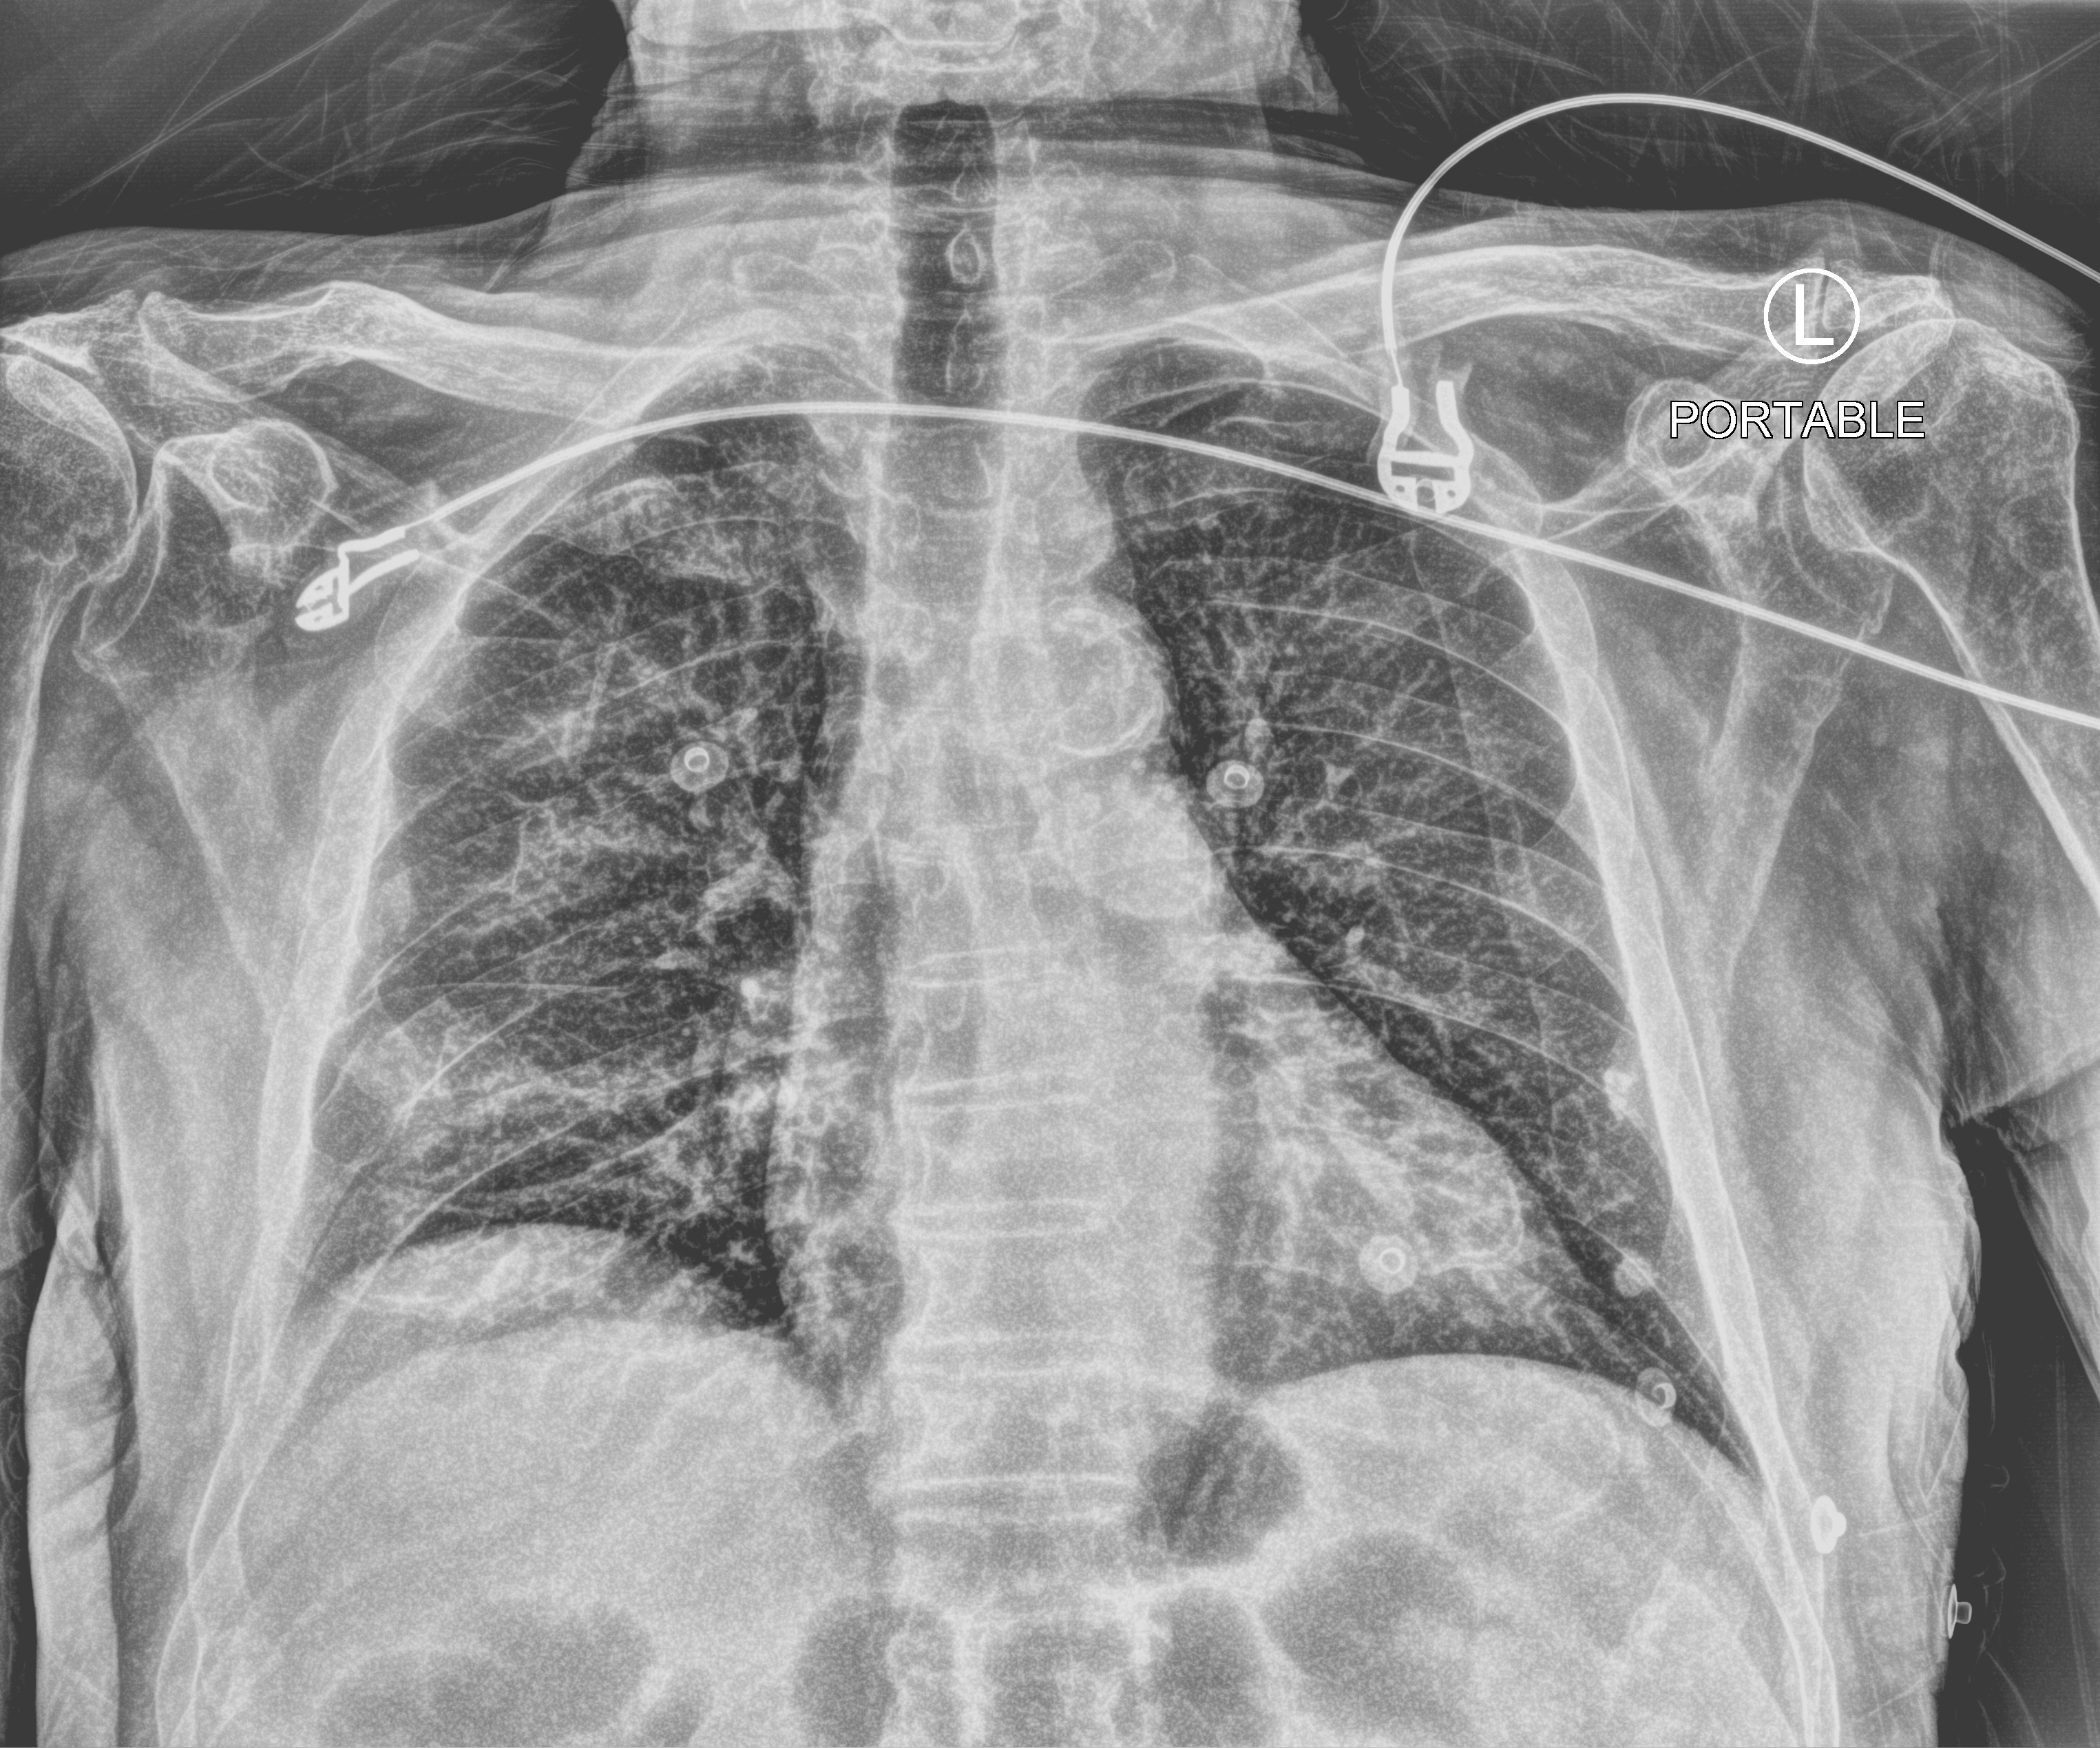
Portable chest radiograph; anteroposterior (AP) projection. Patient hospitalised with COVID-19; male, aged 75–90 years.
From the hospital-stay record, not from the radiograph (when in the stay this image was taken is not recorded): chronic kidney disease (admission record): no; admitted to intensive care during this hospital stay: no; mechanically ventilated during this hospital stay: no.